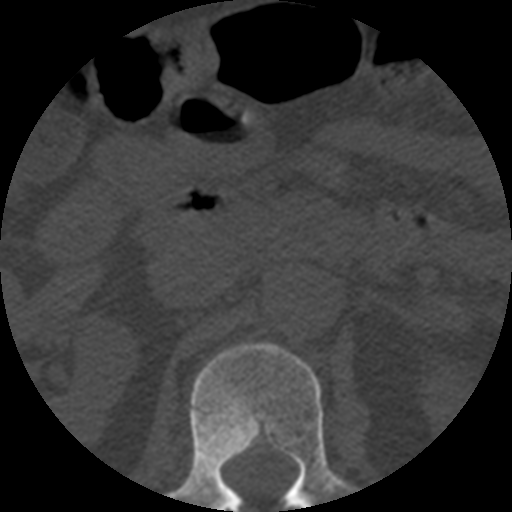
CT including the spine, one axial slice. Position 185 of 508 along the scan axis. Bone window (W 1800 / L 400 HU). 1.25 mm slice thickness. 512 × 512 image matrix, field of view 160 × 160 mm. Patient age 57 years. From the clinical record (not read from this slice): primary cancer: prostate.
Structures marked on this image (semi-automatically segmented with operator editing):
- L1 vertebra: bounding box [x1, y1, x2, y2] px = [170, 343, 354, 512]